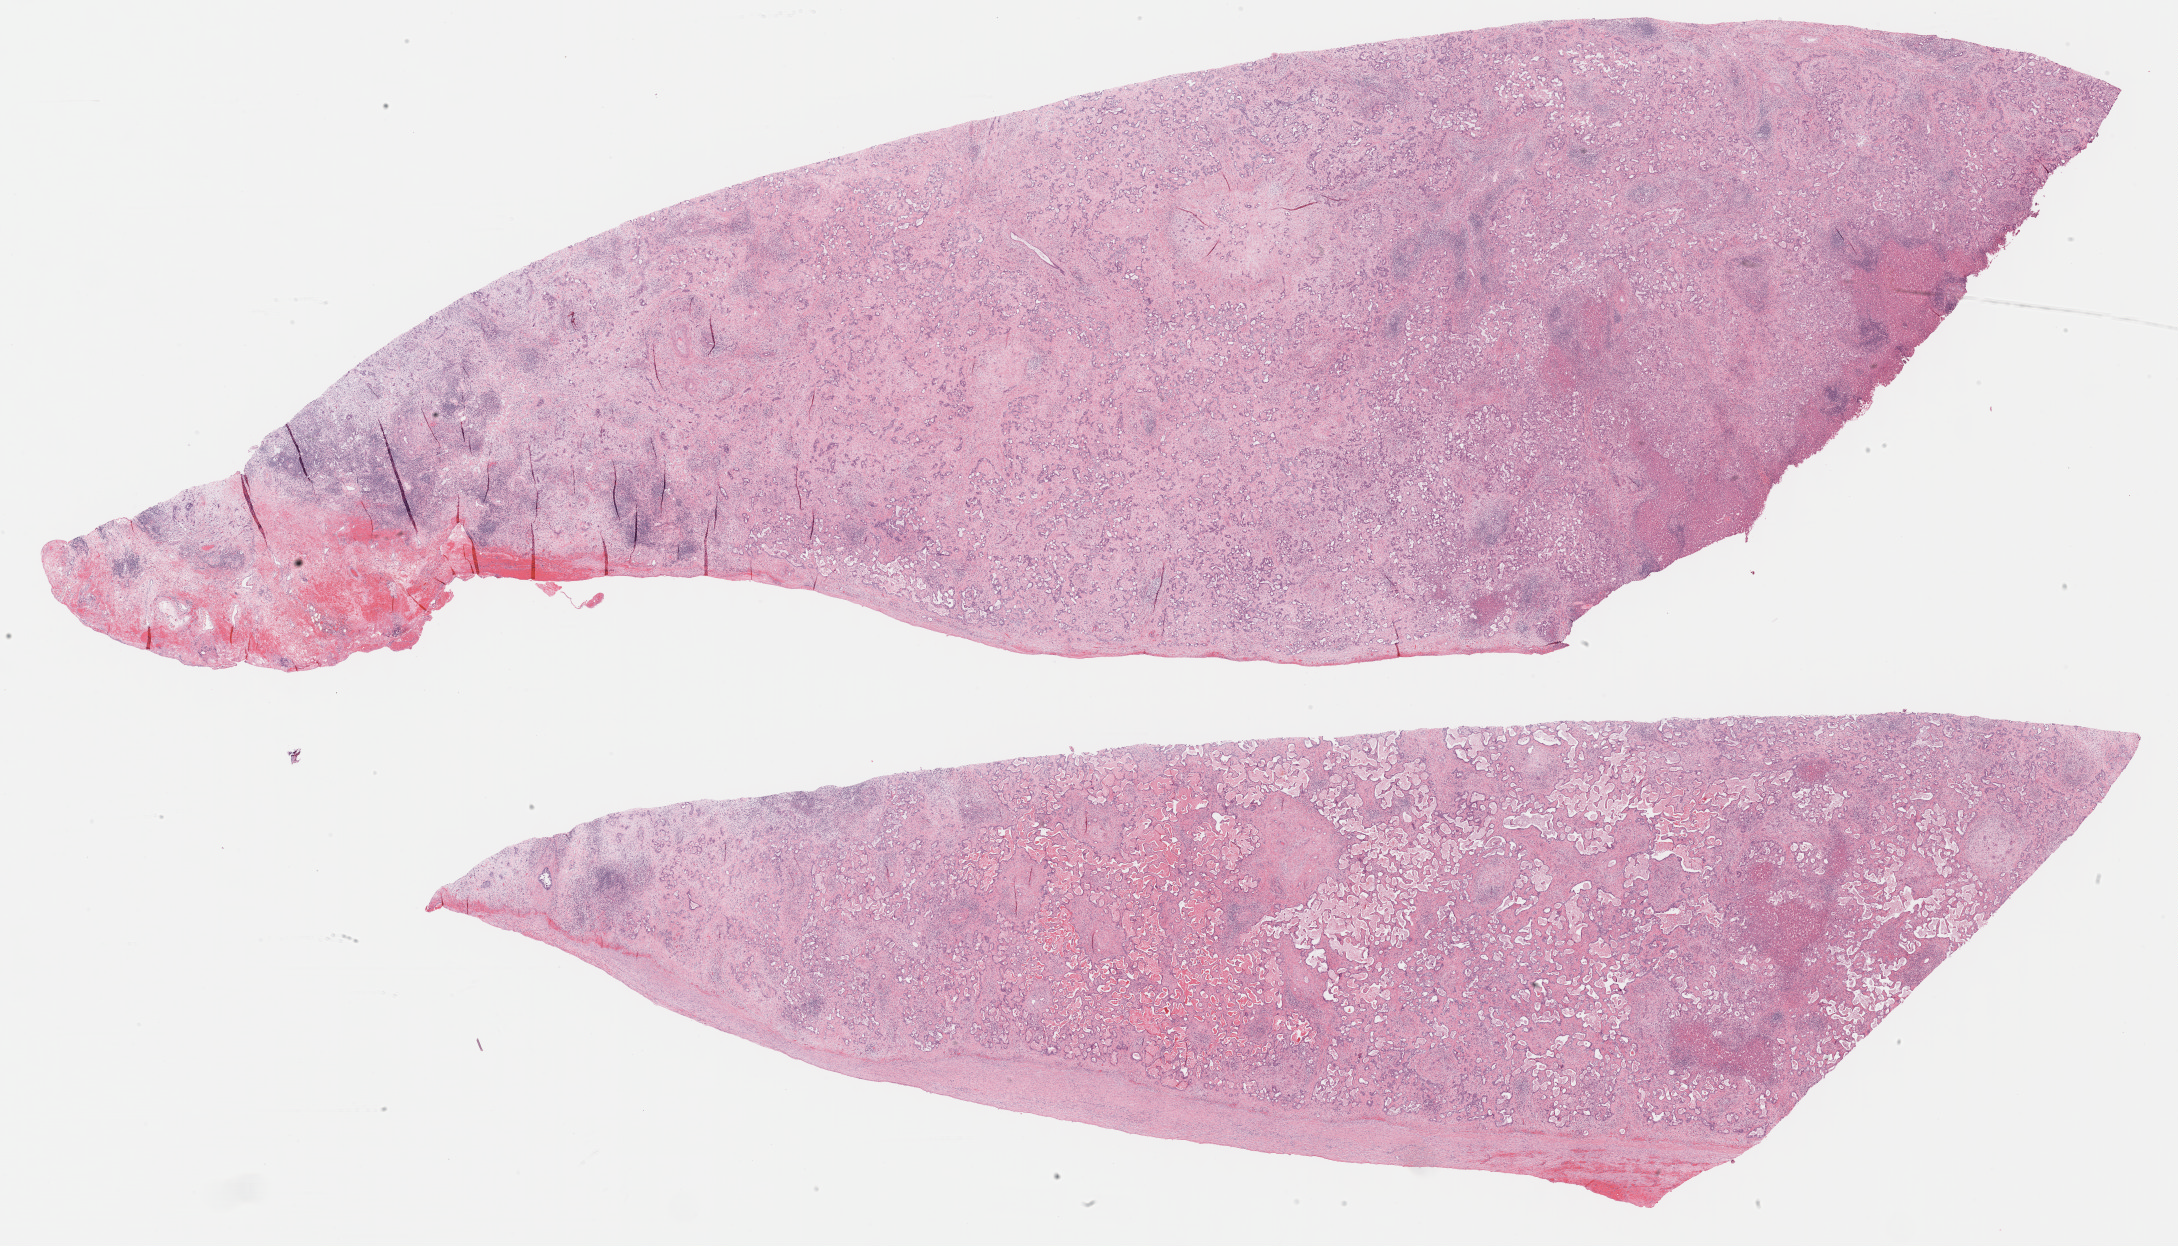
Digitized H&E tissue section (whole slide) — low-resolution overview of the scanned area, about 35.2 x 20.2 mm (acquisition: 40x scan), formalin-fixed paraffin-embedded (FFPE) diagnostic section, bile duct, primary tumour sample. Male, age 72 years at initial diagnosis. Histologic grade: G2 (moderately differentiated).
Diagnosis: Cholangiocarcinoma (intrahepatic bile duct). AJCC pathologic stage: I.